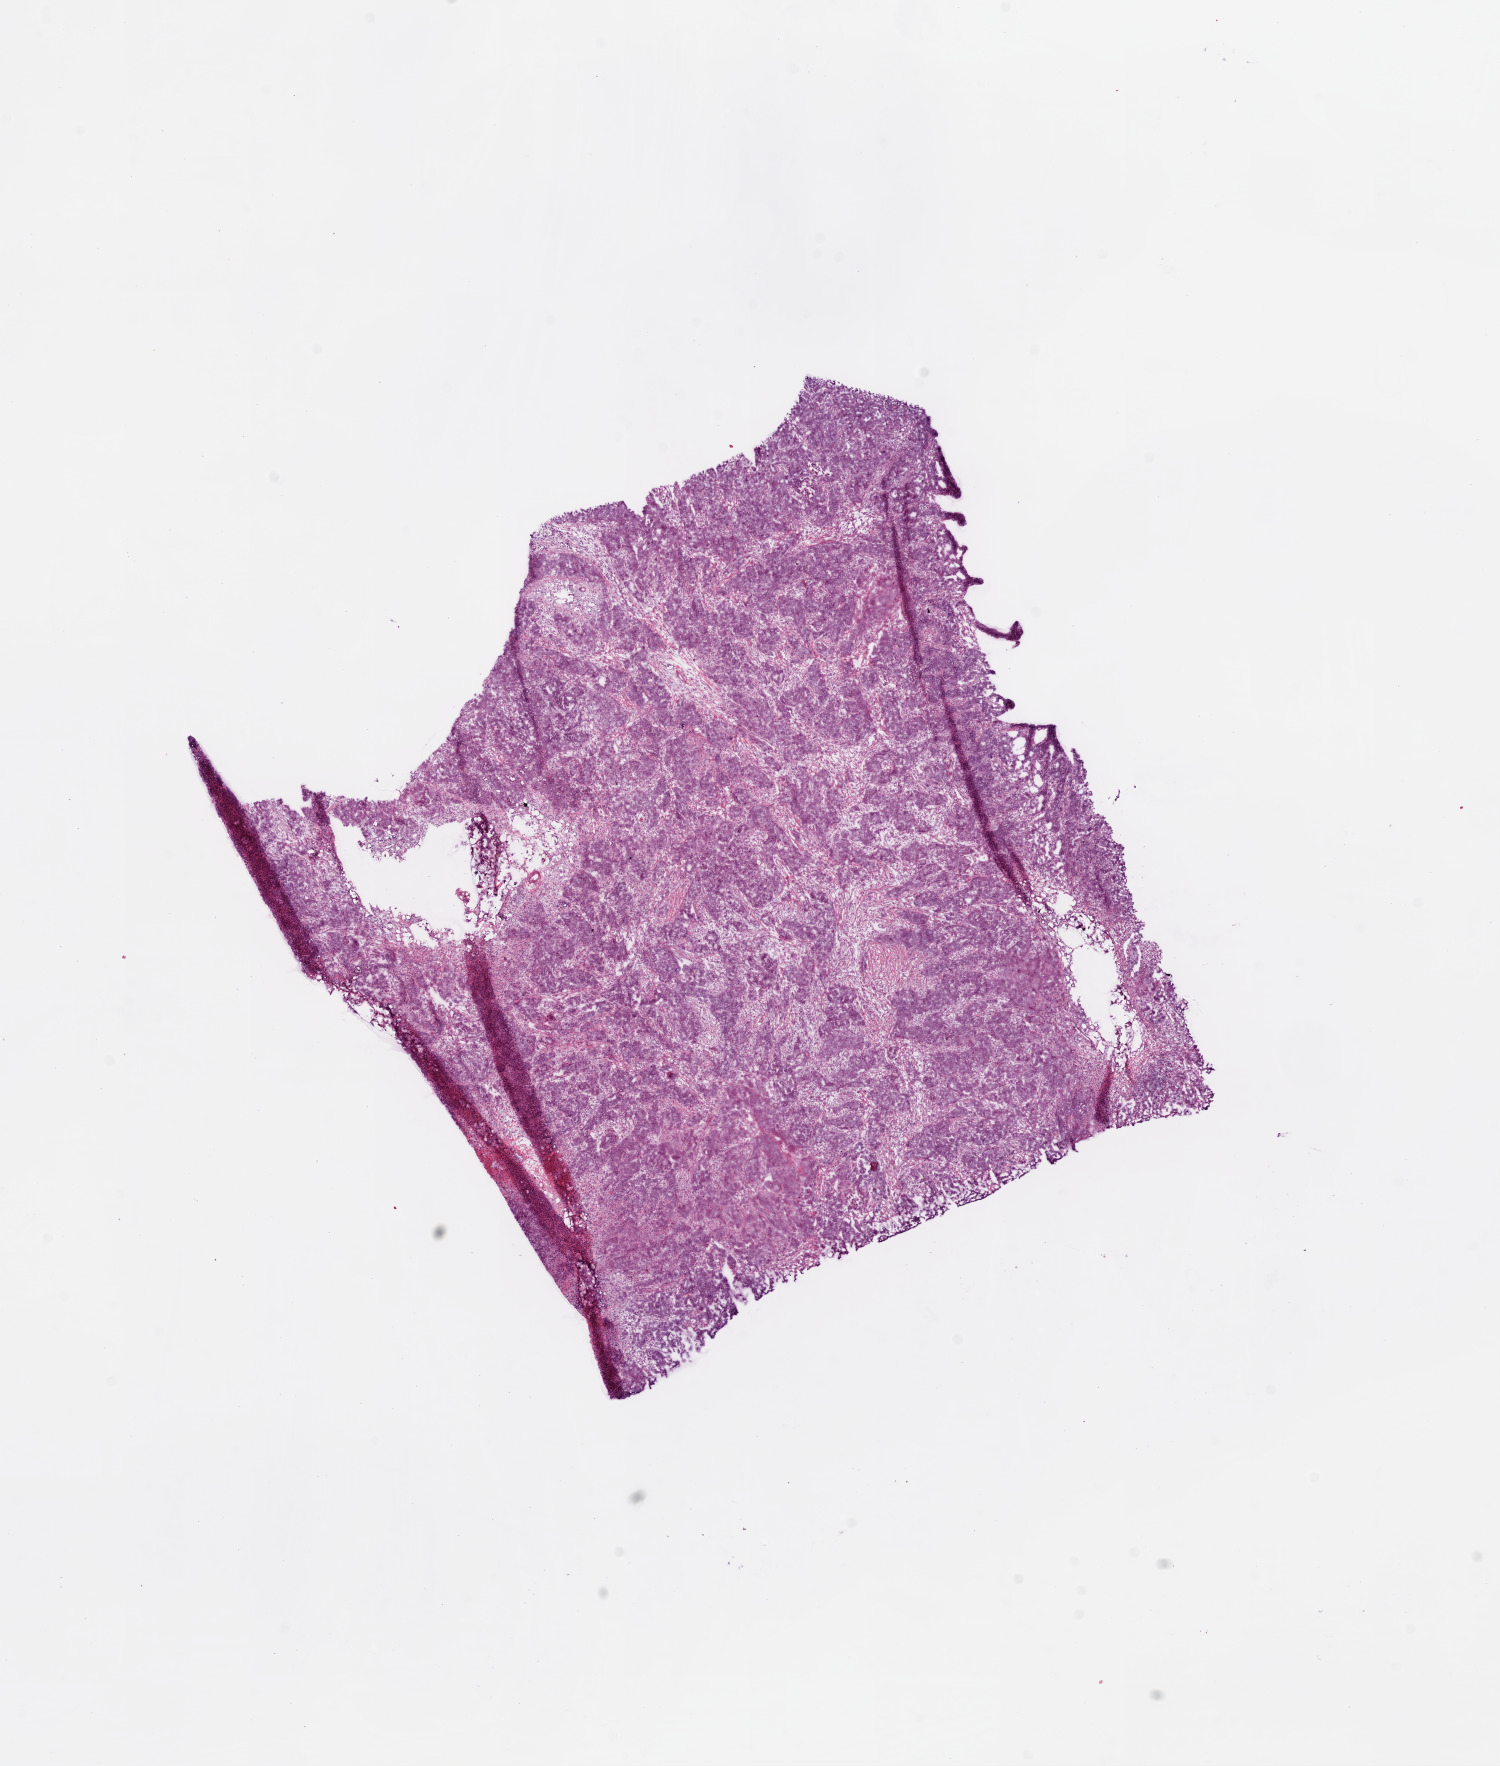
Whole-slide histology image, H&E, shown as a low-resolution overview of the whole scanned area (about 12.0 x 14.2 mm, from a 20x scan). Frozen section. Ovary, primary tumour sample. Patient: female, age at initial diagnosis 49 years. Histologic grade: G3 (poorly differentiated). Slide review estimates, as recorded: tumour cells 70%, tumour nuclei 80%, normal cells 0%, stromal cells 30%, necrosis 0%.
FIGO stage: IIIC. Laterality: bilateral. Pathologic diagnosis: Serous cystadenocarcinoma, NOS.